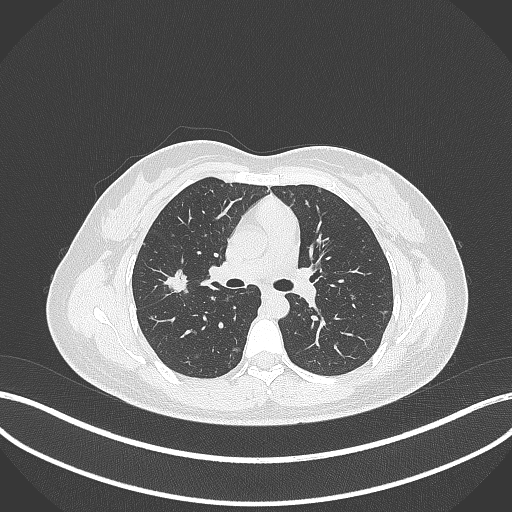
Chest CT, one axial slice; slice 200 of 307 in the series (ordered by position); reconstruction kernel B70f; 120 kVp; lung window (W 1500 / L -600 HU); 512 × 512 image matrix, field of view 400 × 400 mm. Female patient, age 33 years. Case-level facts recorded for this patient, not image findings: clinical TNM (as recorded): T1c N0 M0; histopathological grade: G2-G3.
Outlined on this slice (bounding box drawn by a radiologist):
- lung tumour (recorded histology: adenocarcinoma): box from (x=158, y=266) to (x=197, y=297) px